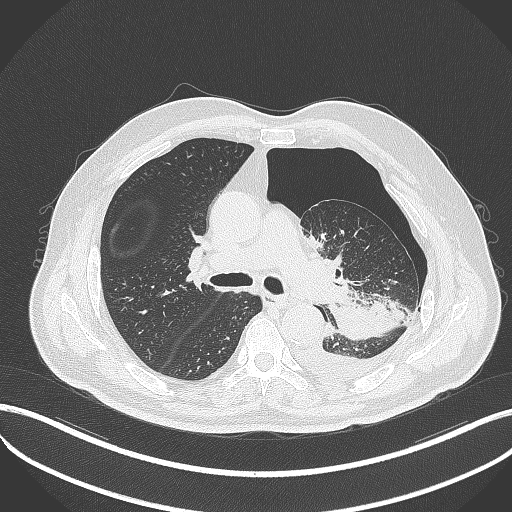
Chest CT, one axial slice; position 320 of 464 along the scan axis; reconstruction kernel B70f; 120 kVp; lung window (W 1500 / L -600 HU); 1 mm slice thickness; 512 × 512 image matrix, field of view 400 × 400 mm. Patient: male, 76 years. Case-level facts recorded for this patient, not image findings: clinical TNM (as recorded): T3 N0 M1b.
Outlined on this slice (bounding box drawn by a radiologist):
- lung tumour (recorded histology: adenocarcinoma): box from (x=323, y=287) to (x=402, y=340) px